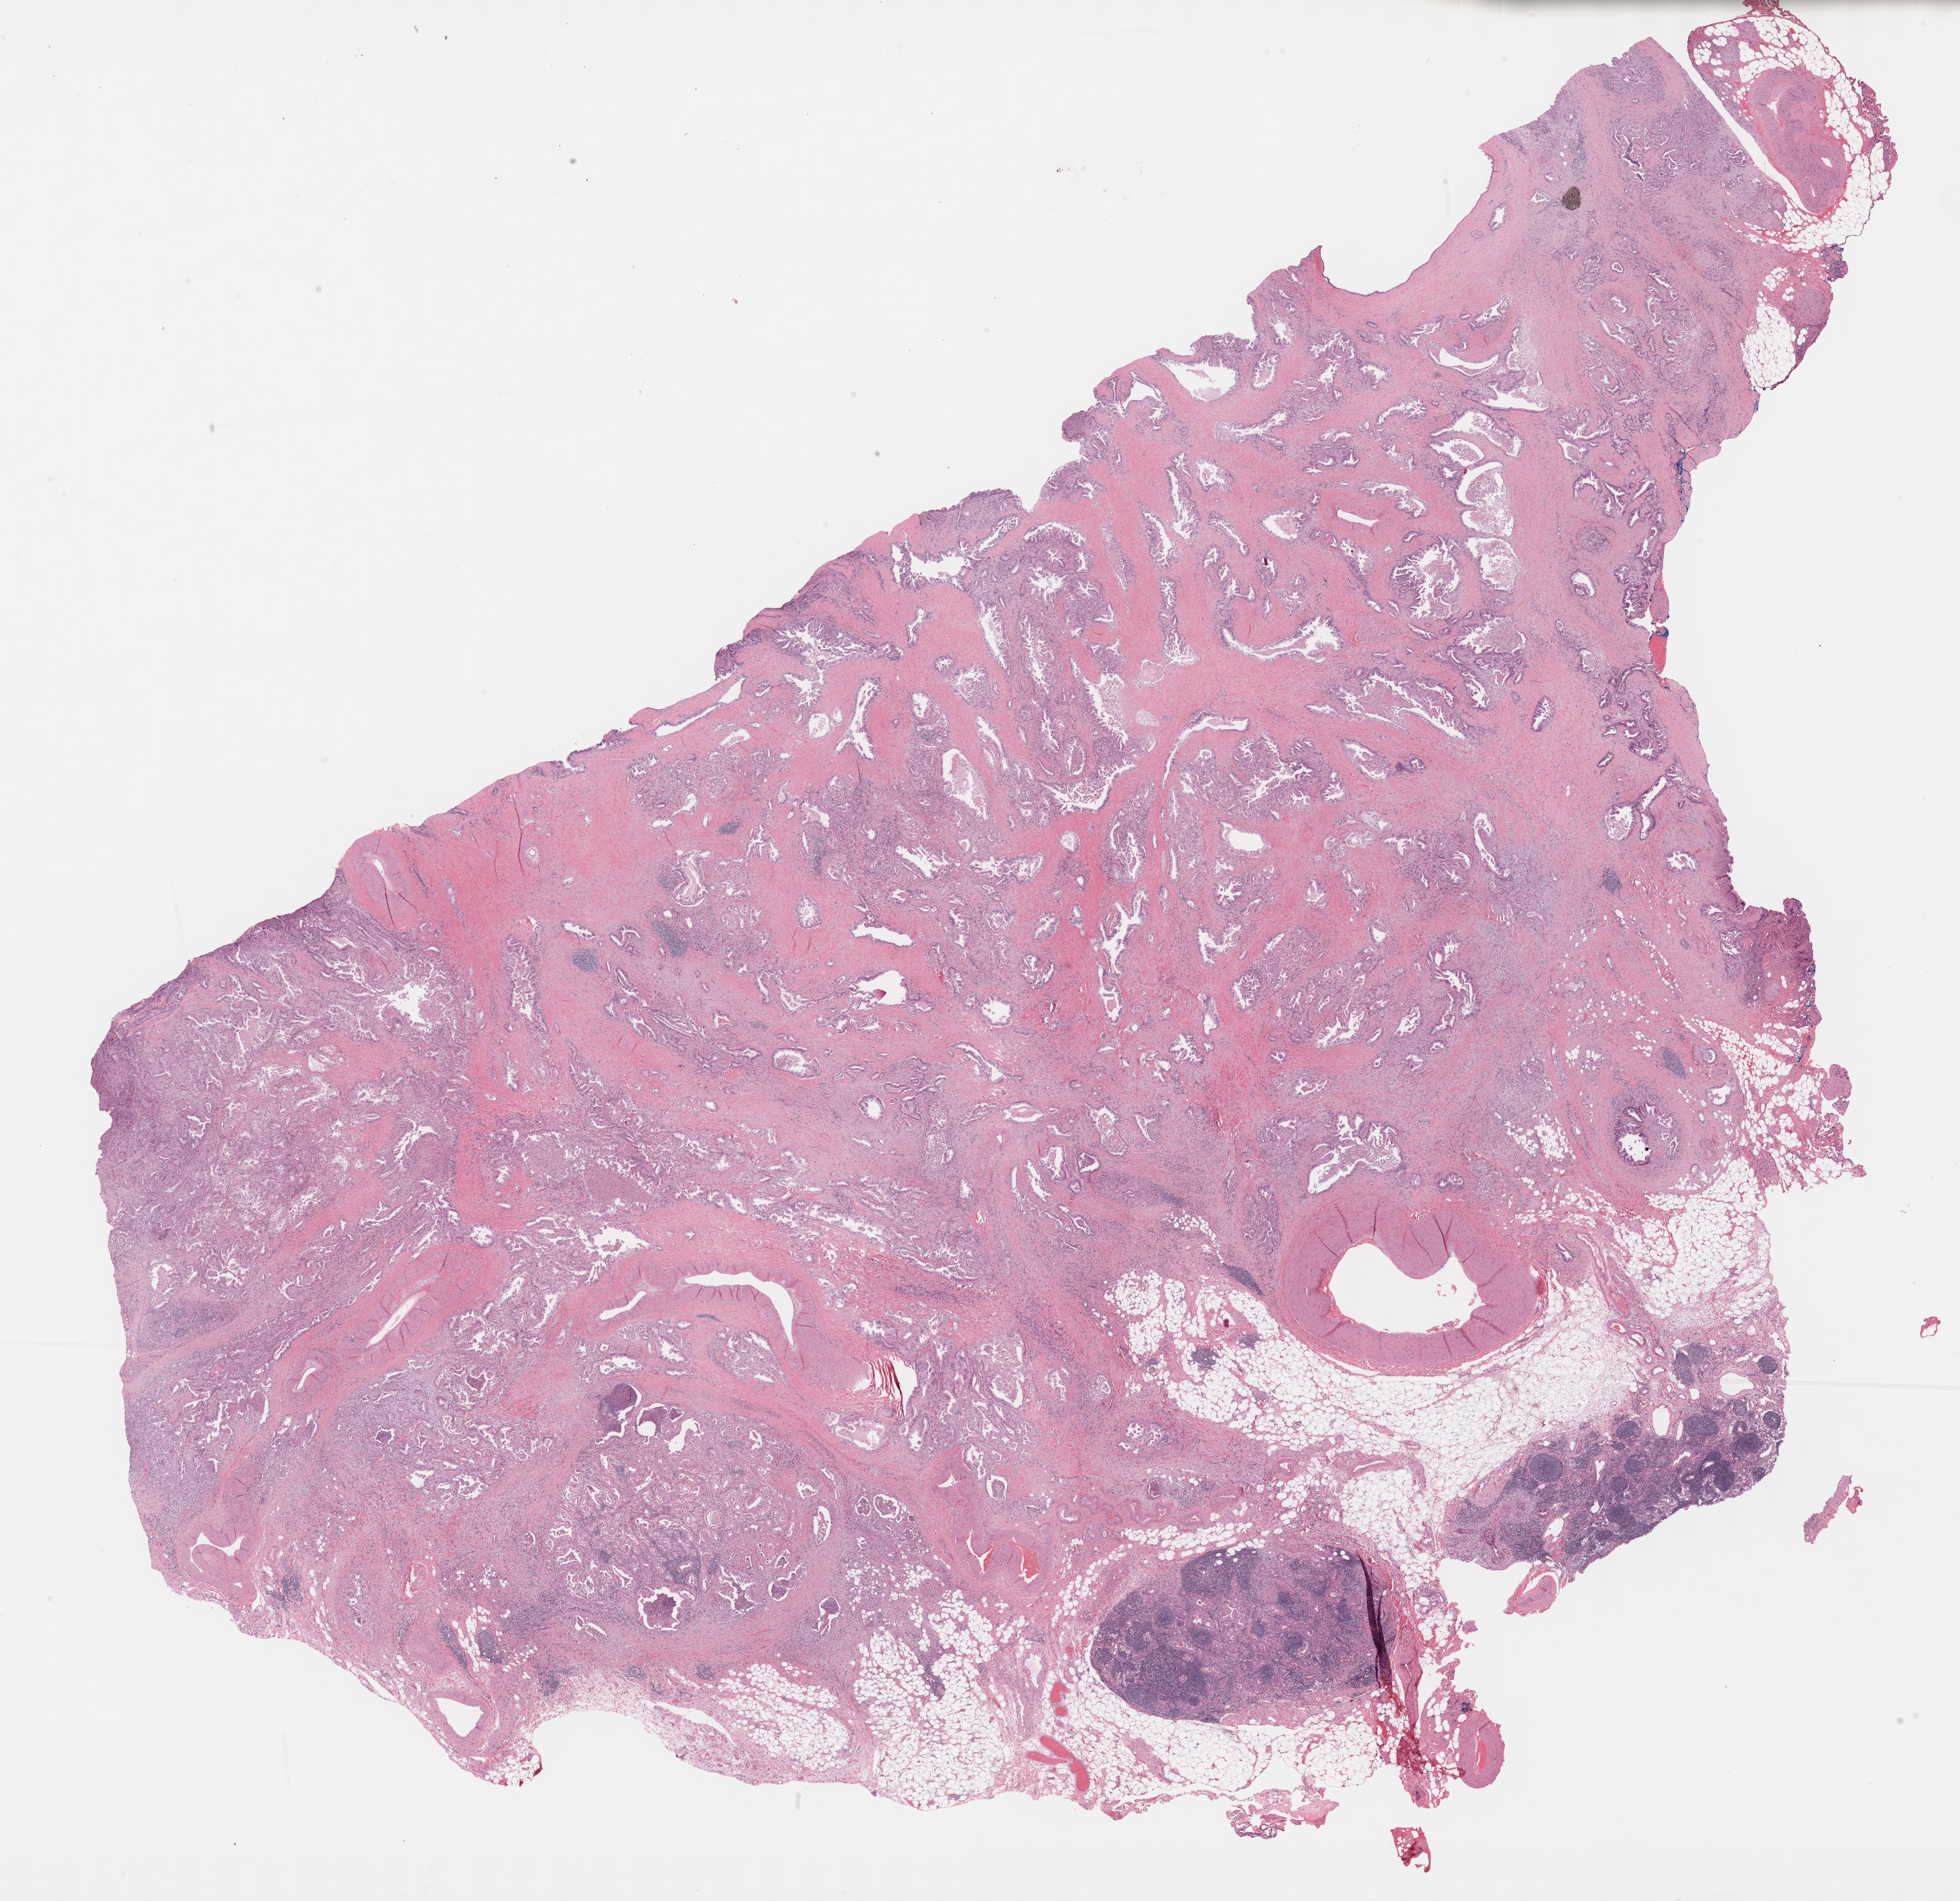
Whole-slide histology image, H&E-stained — a low-resolution overview of the entire scanned area, about 23.7 x 22.9 mm (from a 40x scan). Formalin-fixed paraffin-embedded (FFPE) diagnostic section. Sample: primary tumour, pancreas. Patient: female, age at initial diagnosis 79 years. Histologic grade: G1 (well differentiated).
TNM: T4 N1 M0. Histologic diagnosis: Infiltrating duct carcinoma, NOS (head of pancreas). Lymph nodes positive (case pathology): 5 of 10 examined. AJCC pathologic stage: III.